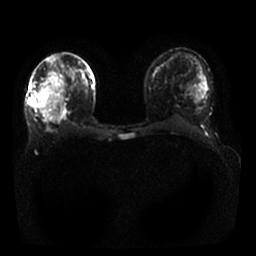
Breast MRI, one axial slice; position 6 of 25 along the scan axis; diffusion-weighted series; image 2 of 4 stored at this slice position (different b-values; order by instance number); 1.5 T; 256 × 256 image matrix, field of view 330 × 330 mm. Female patient.
Annotated regions visible in this slice (manually delineated by an expert):
- tumour on diffusion-weighted imaging: bounding box <29,98,36,104> (left, top, right, bottom; pixels)